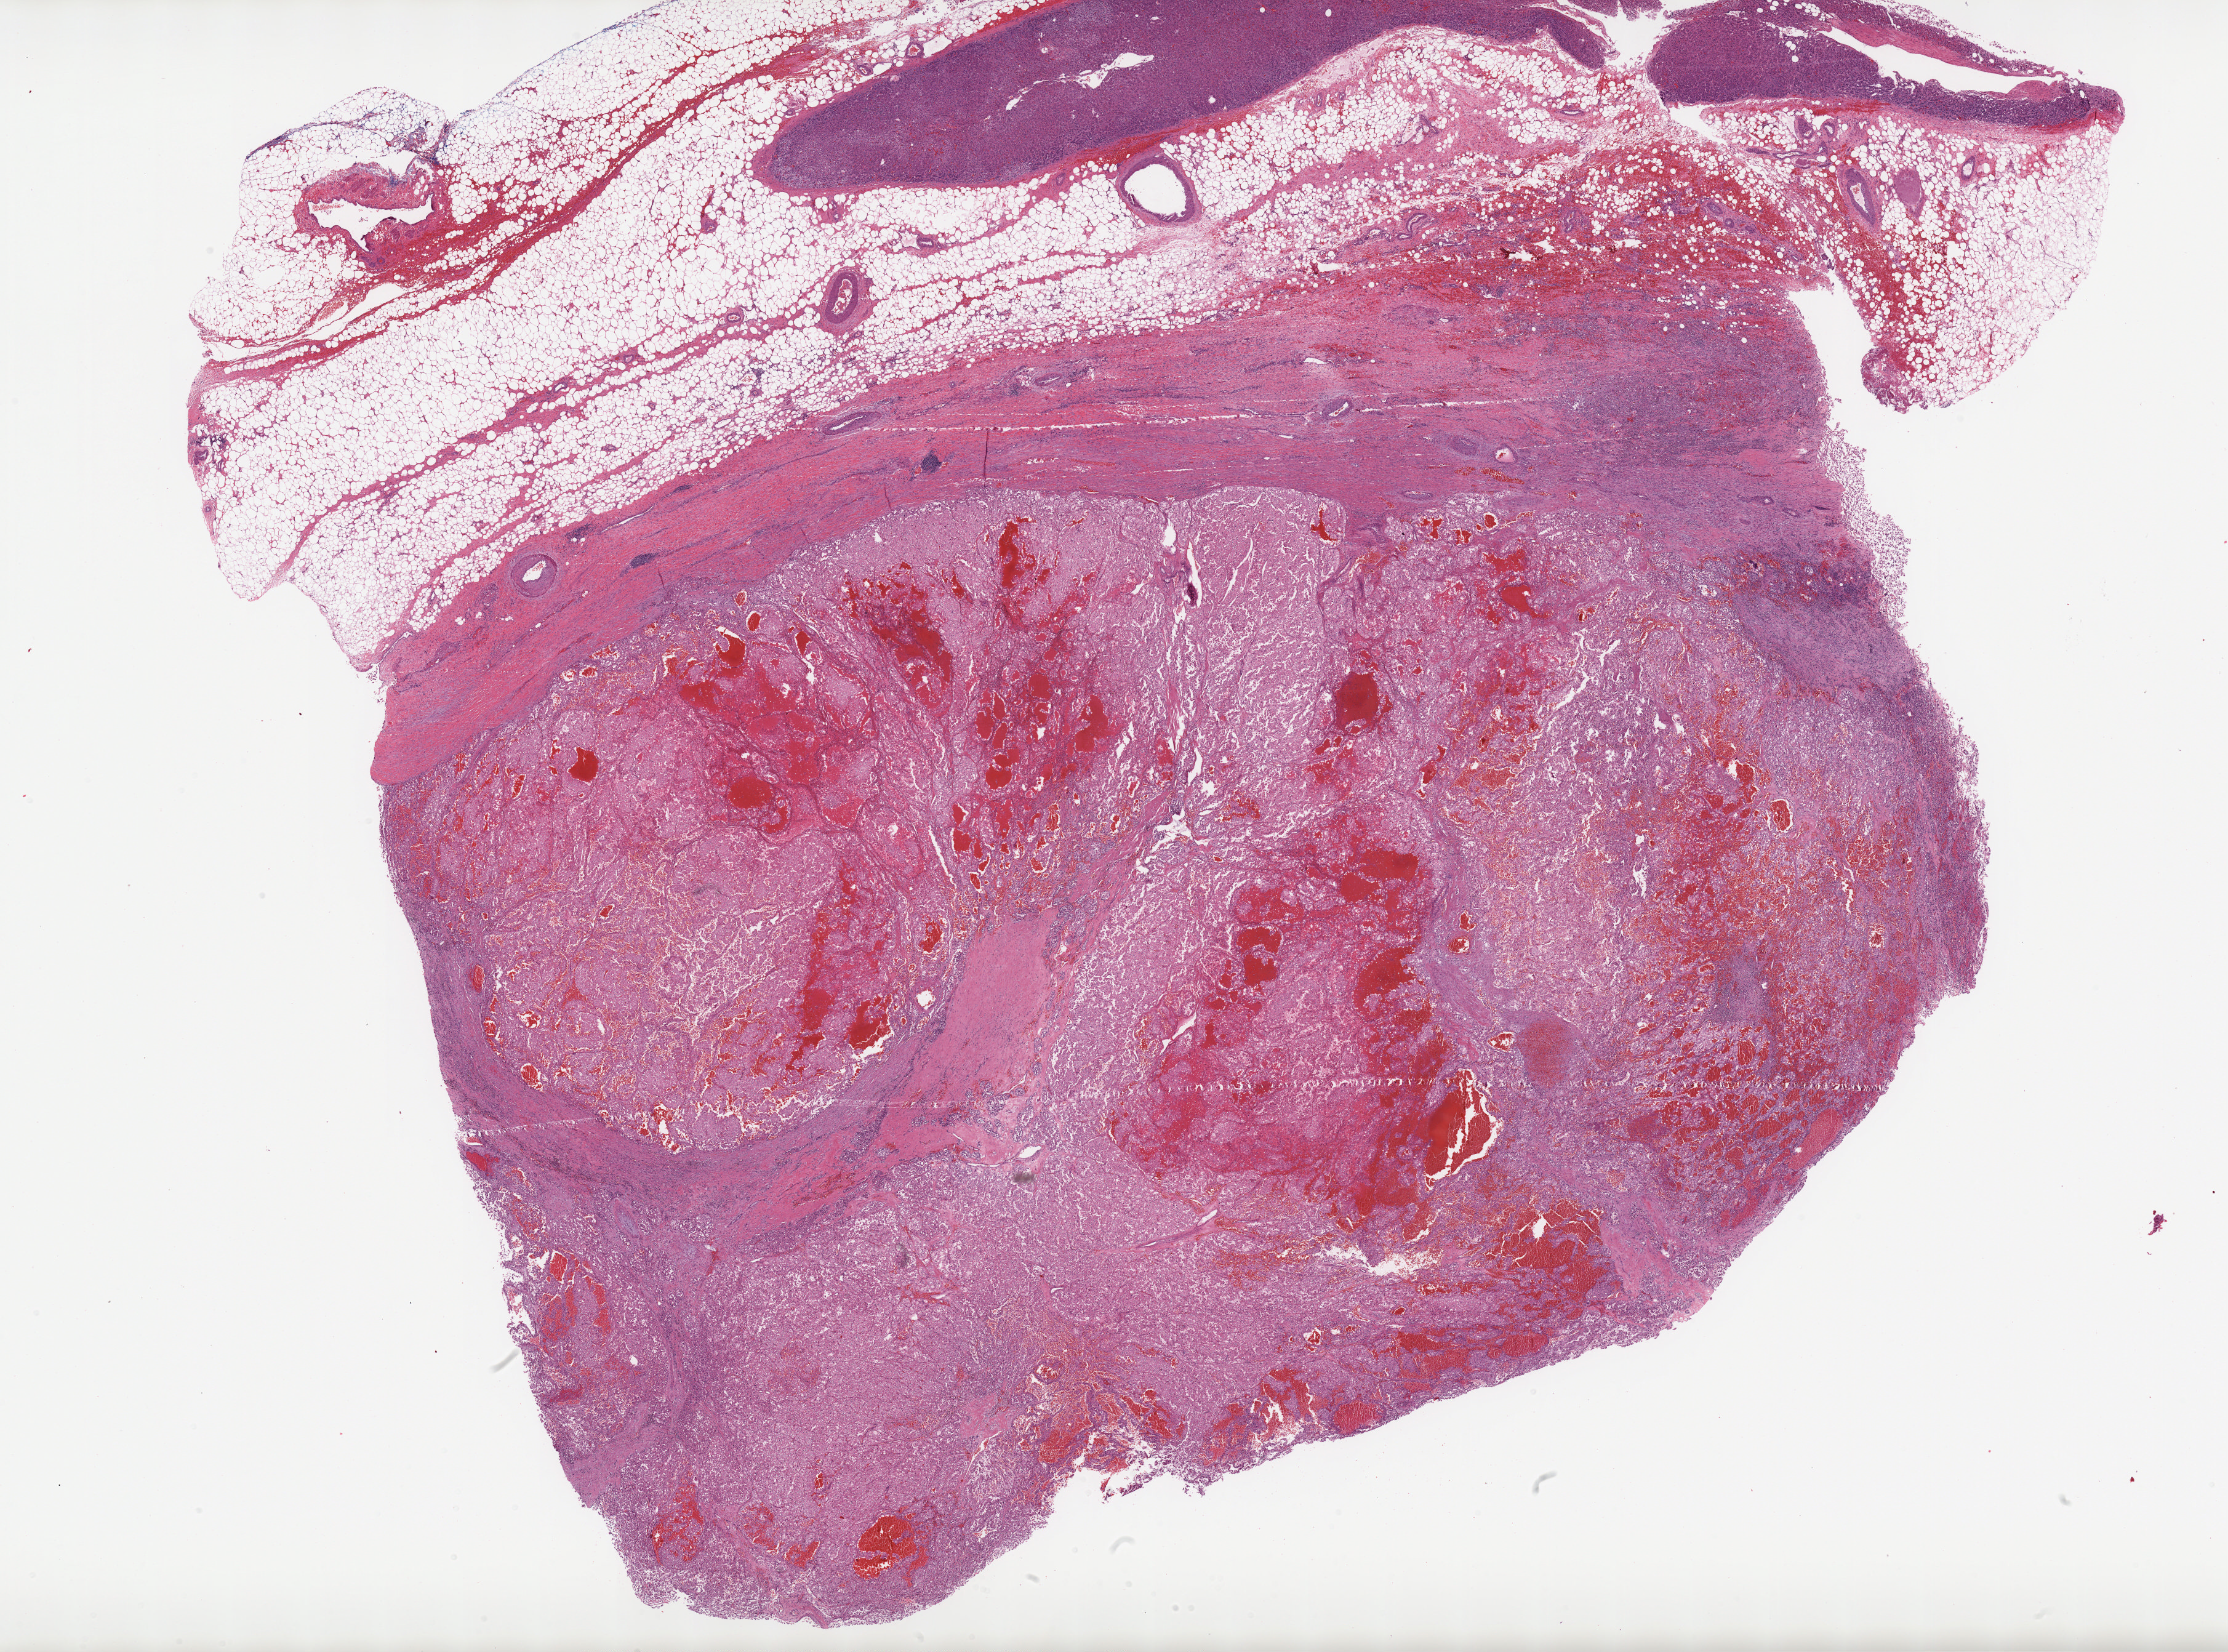
Hematoxylin and eosin (H&E) stained whole-slide image, whole scanned area (about 28.8 x 21.4 mm) shown as a low-resolution overview; formalin-fixed paraffin-embedded (FFPE) diagnostic section; primary tumour sample from the kidney. Male patient; age at initial diagnosis 67 years.
* AJCC pathologic stage: III (6th edition)
* pathologic diagnosis: Renal cell carcinoma, chromophobe type
* lymph nodes positive (case pathology): 0 of 8 examined